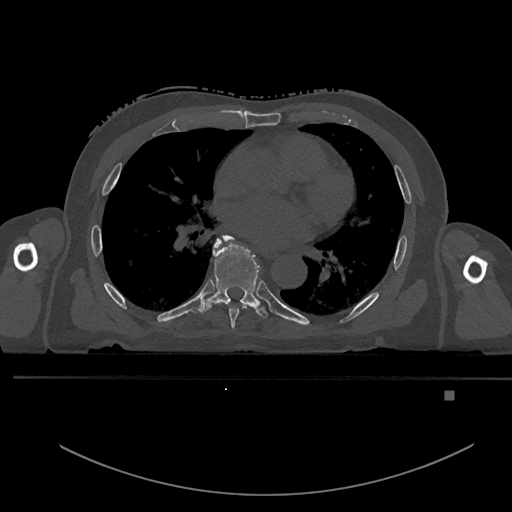
CT including the spine, one axial slice. Position 274 of 969 along the scan axis. Bone window (W 1800 / L 400 HU). 512 × 512 image matrix, field of view 456 × 456 mm. Male patient, age 82 years. Case-level facts recorded for this patient, not image findings: primary cancer: prostate.
Outlined on this slice (semi-automatic segmentation, software-assisted and operator-edited):
- T6 vertebra: box from (x=214, y=239) to (x=249, y=330) px
- T7 vertebra: (x=200, y=235)–(x=268, y=318)